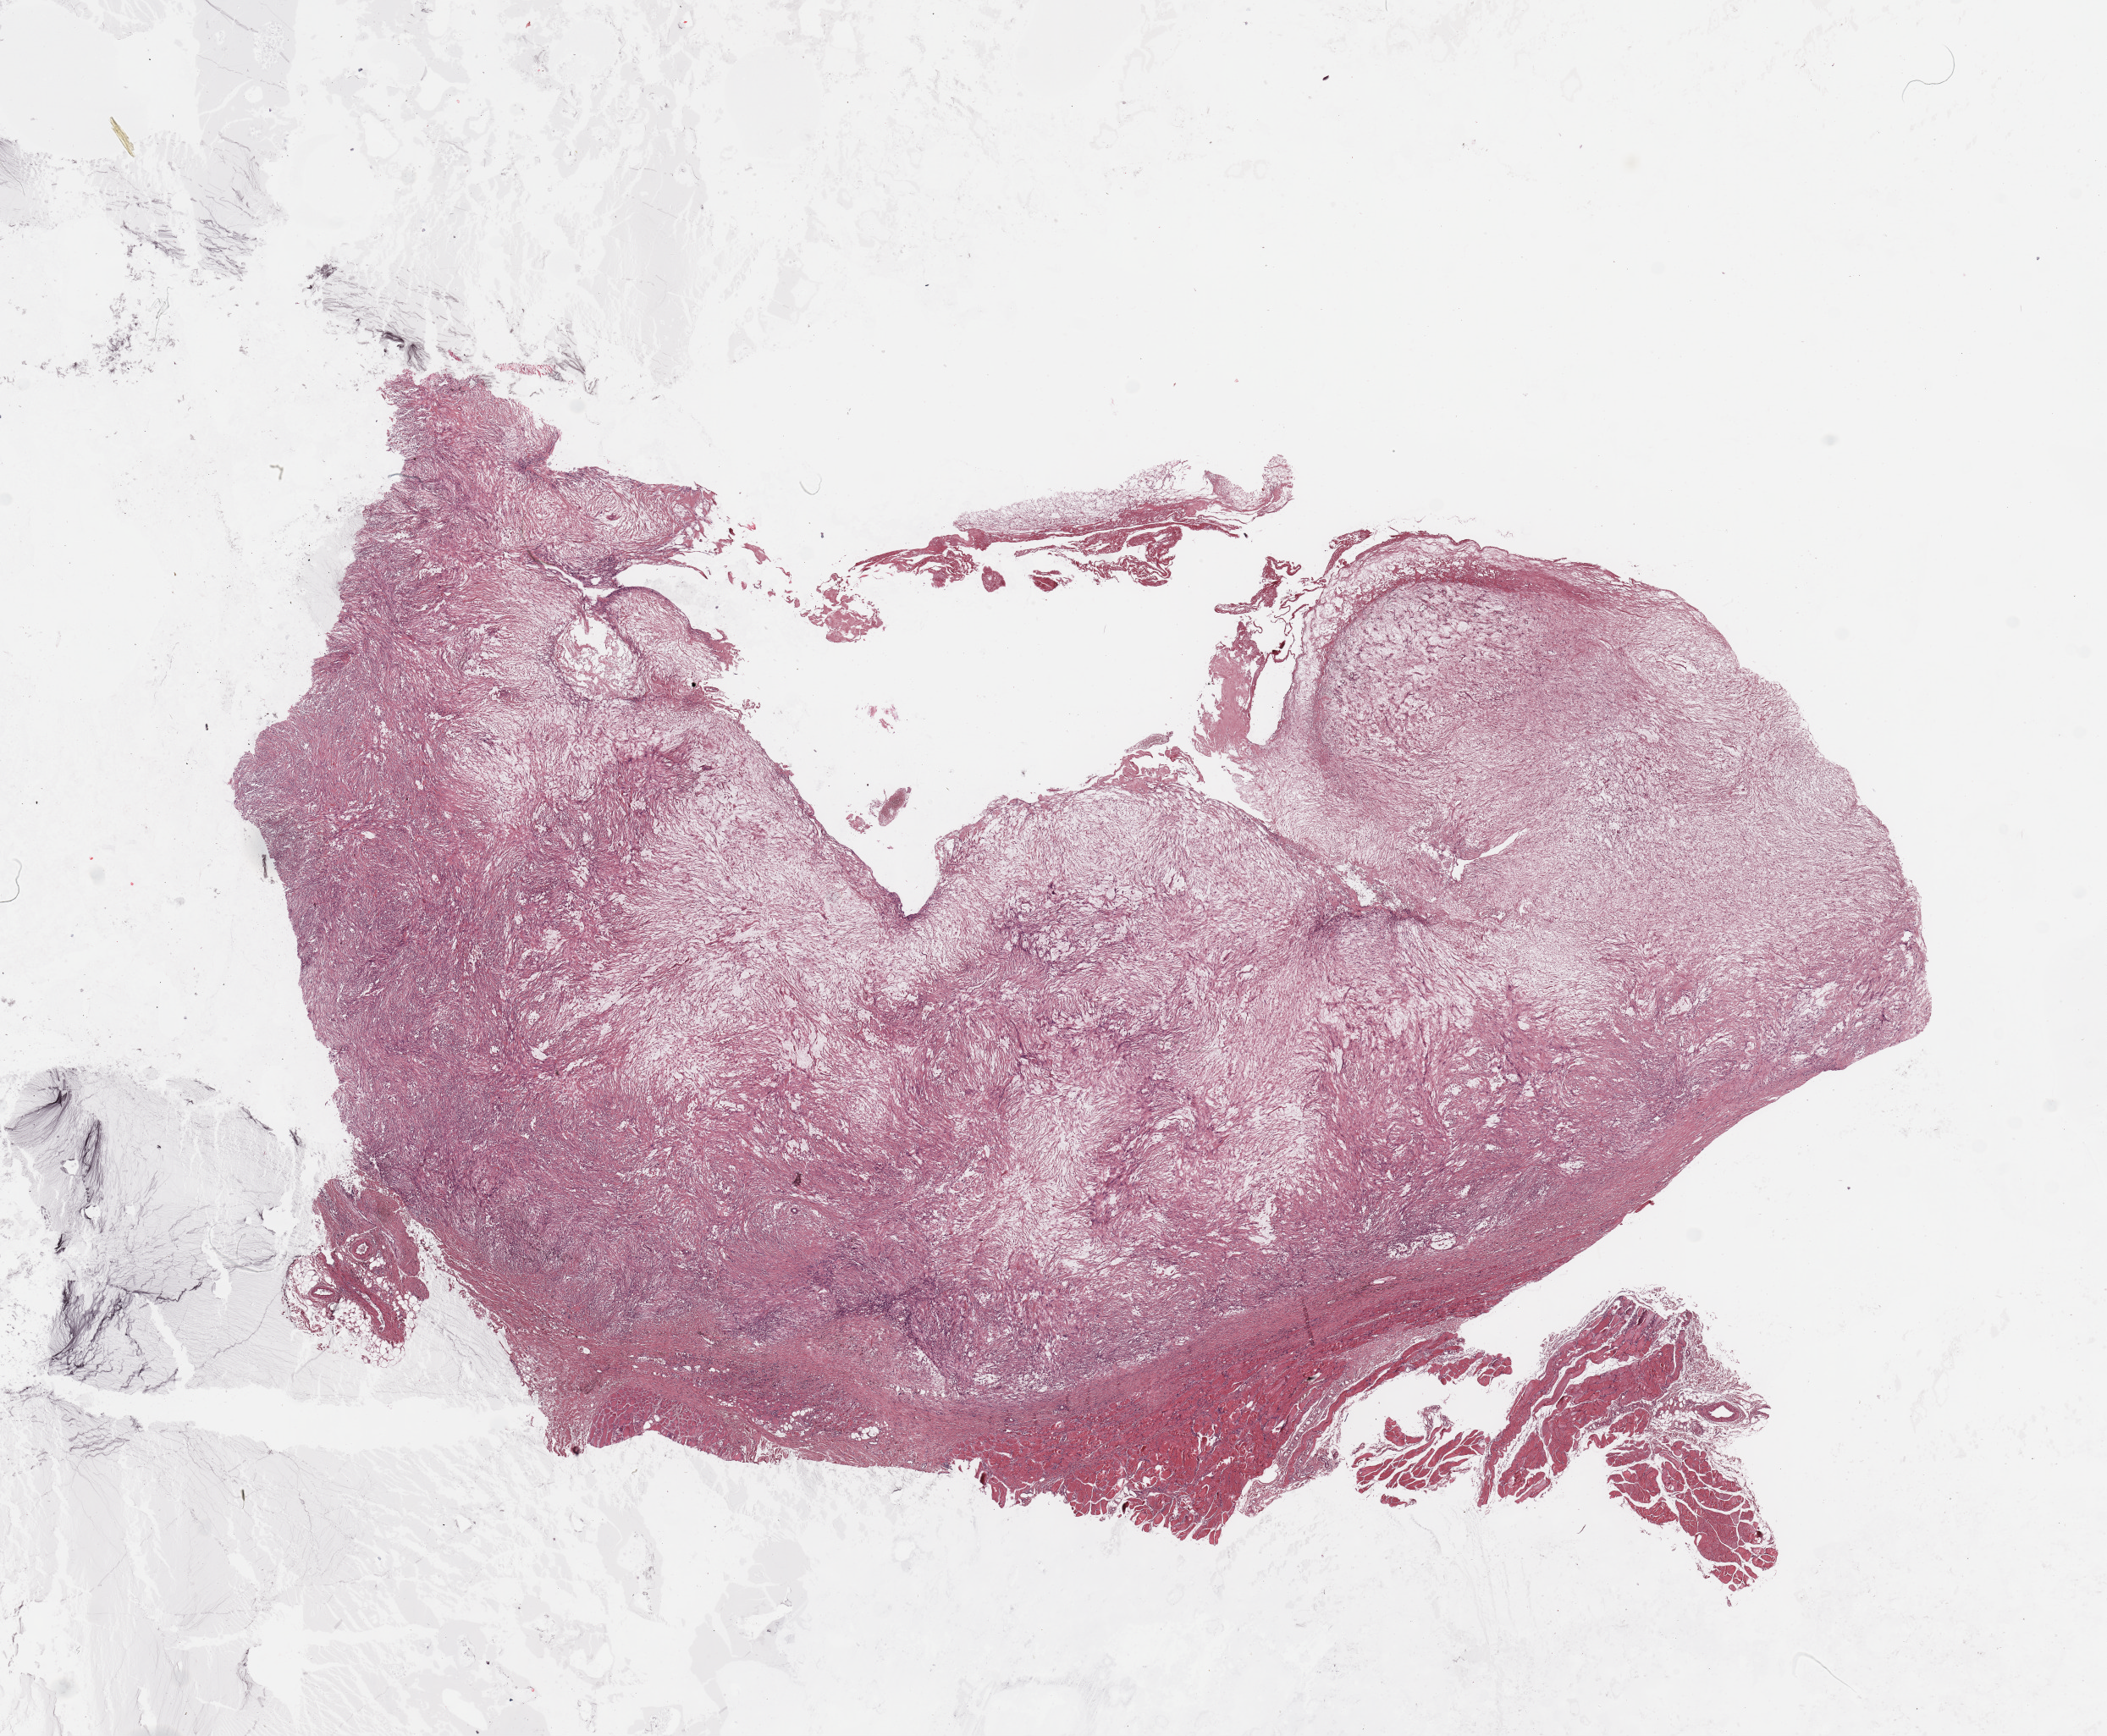
Digitized Hematoxylin and eosin (H&E) stained tissue section (whole slide), a low-resolution overview of the entire scanned area, about 19.7 x 16.2 mm (from a 20x scan). Tumour tissue sample. Female, 67 y/o.
• primary tumour site (as recorded): superficial trunk
• patient diagnosis (cohort enrolment): sarcoma (site not recorded at cohort level)